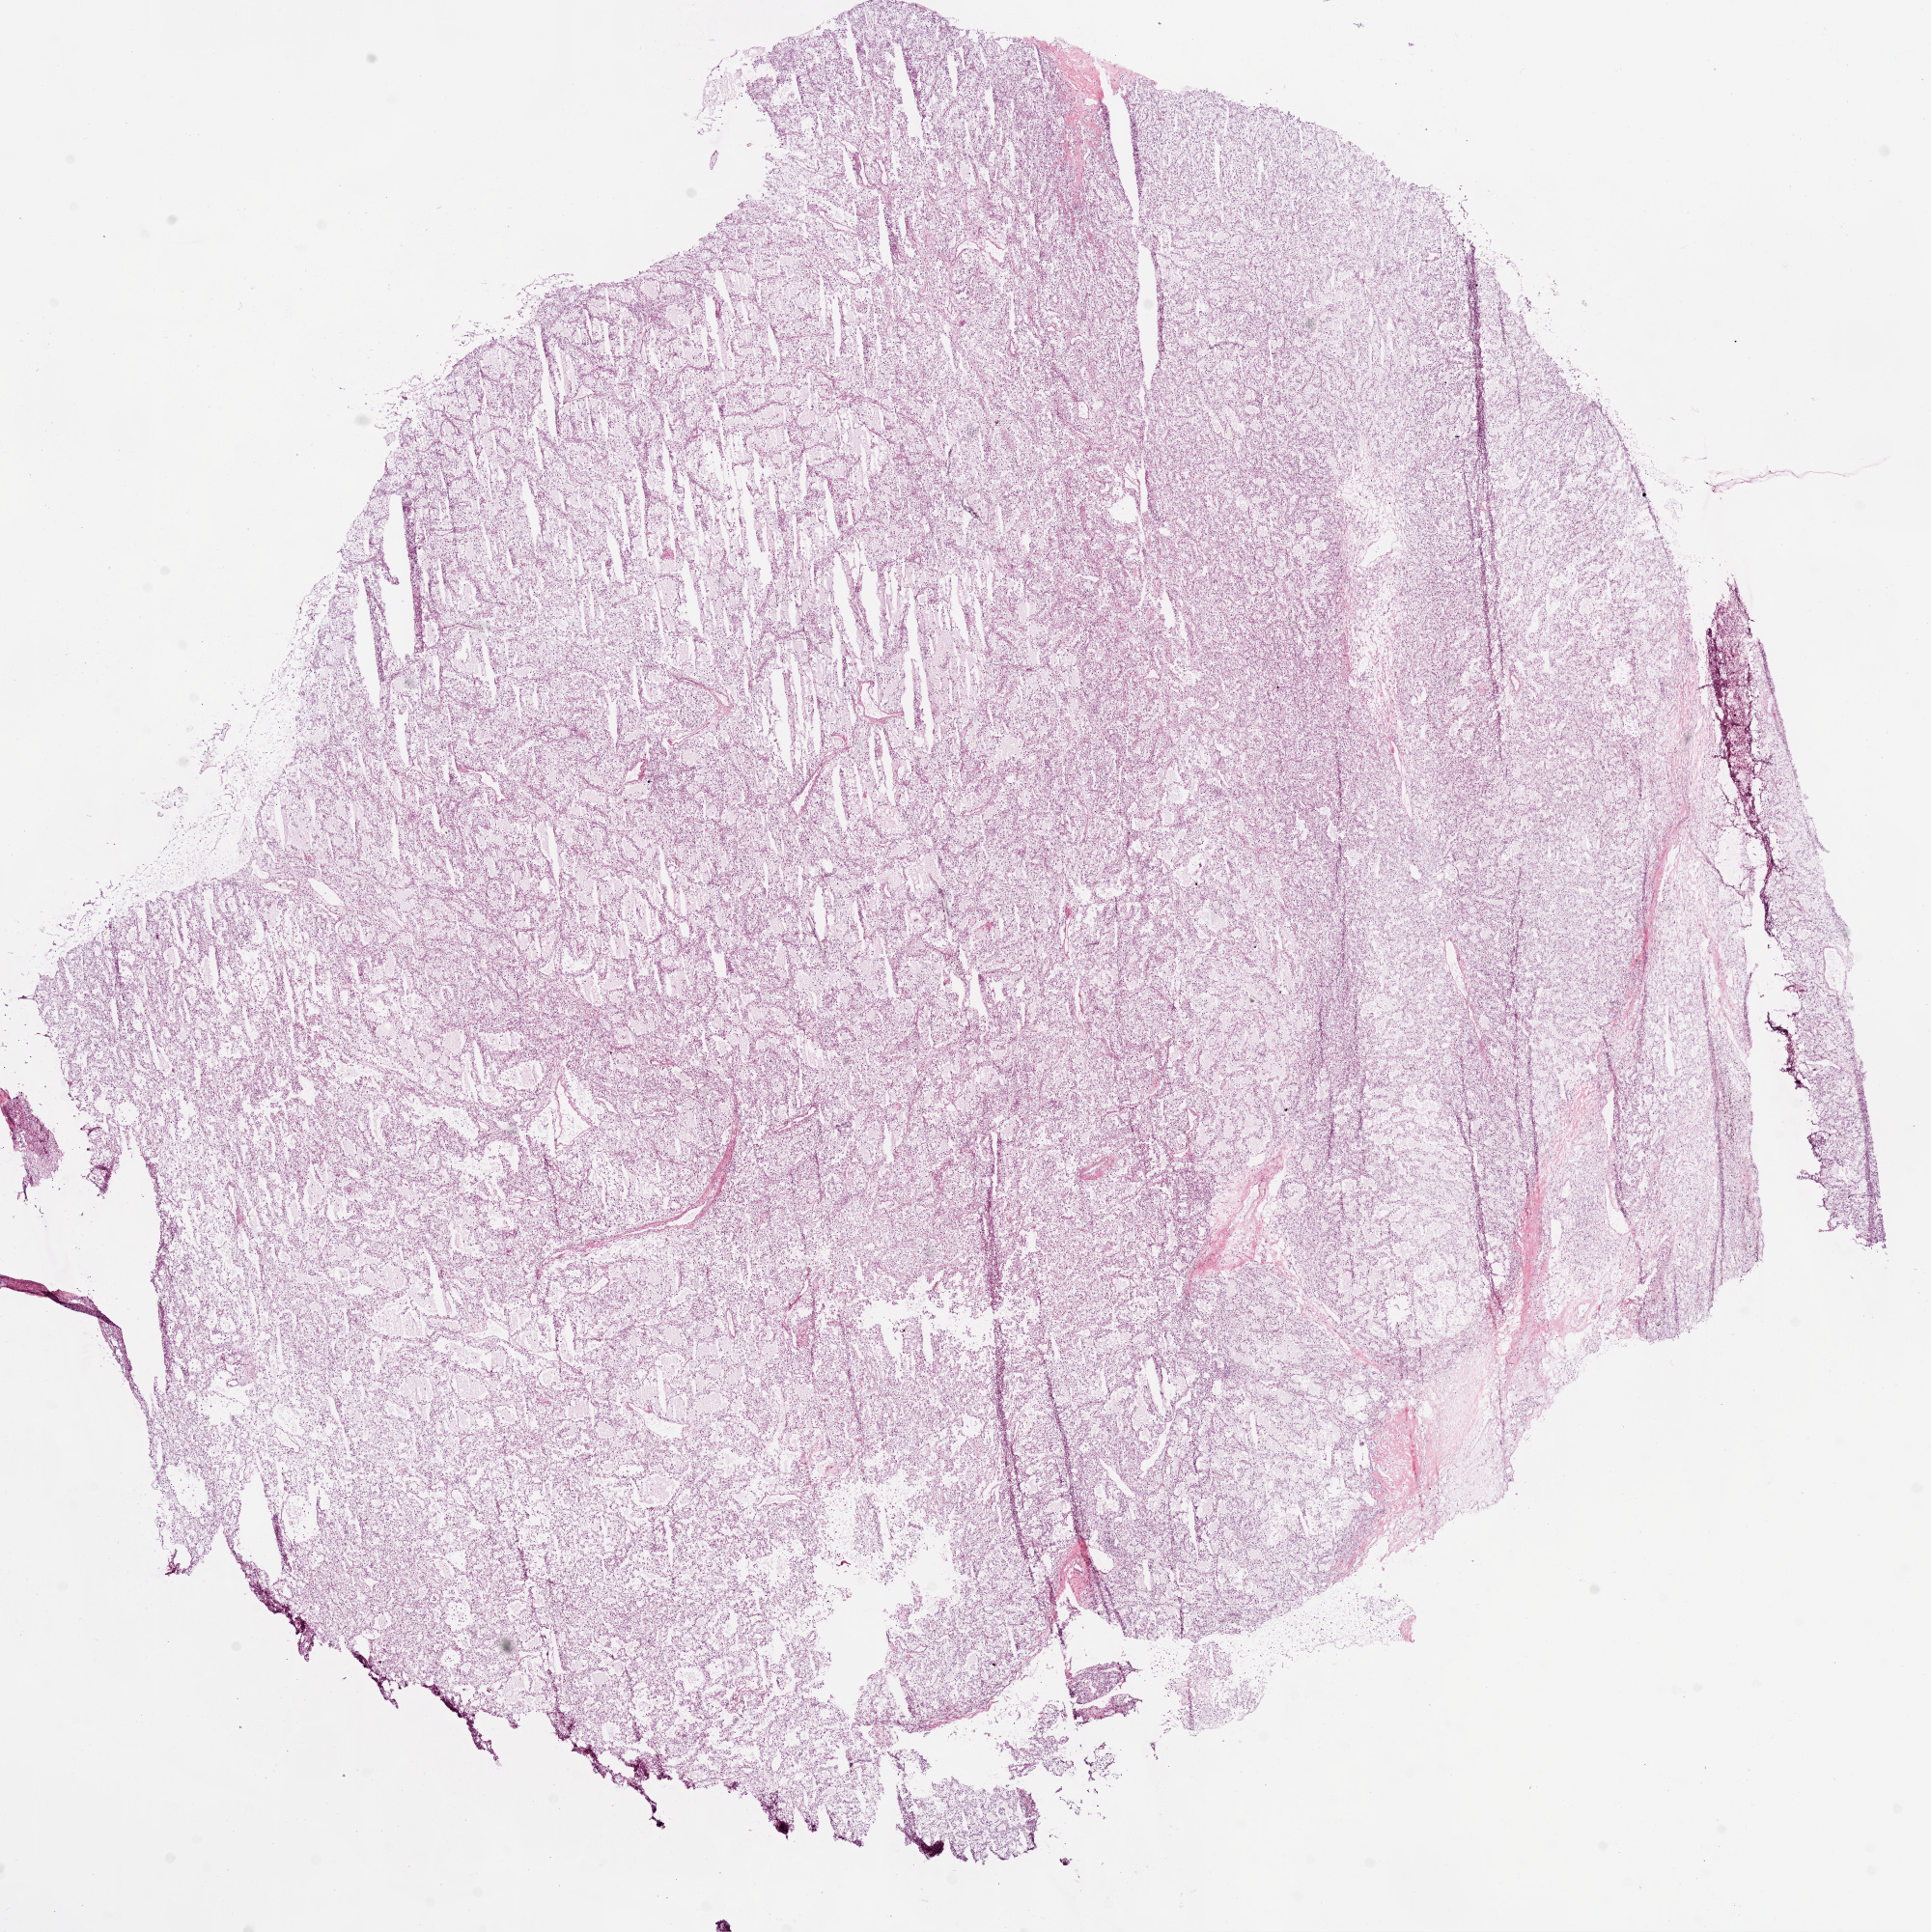
Digitized H&E tissue section (whole slide), low-resolution overview of the scanned area, about 16.0 x 16.1 mm (acquisition: 20x scan); frozen section from the bottom of the tissue portion; sample: primary tumour, kidney. Male patient; age at initial diagnosis 57 years. Histologic grade: G3 (poorly differentiated). Composition of this section per pathologist review: tumour cells 90%, tumour nuclei 85%, normal cells 0%, stromal cells 10%, necrosis 0%.
- histologic diagnosis: Clear cell adenocarcinoma, NOS
- AJCC pathologic stage: I